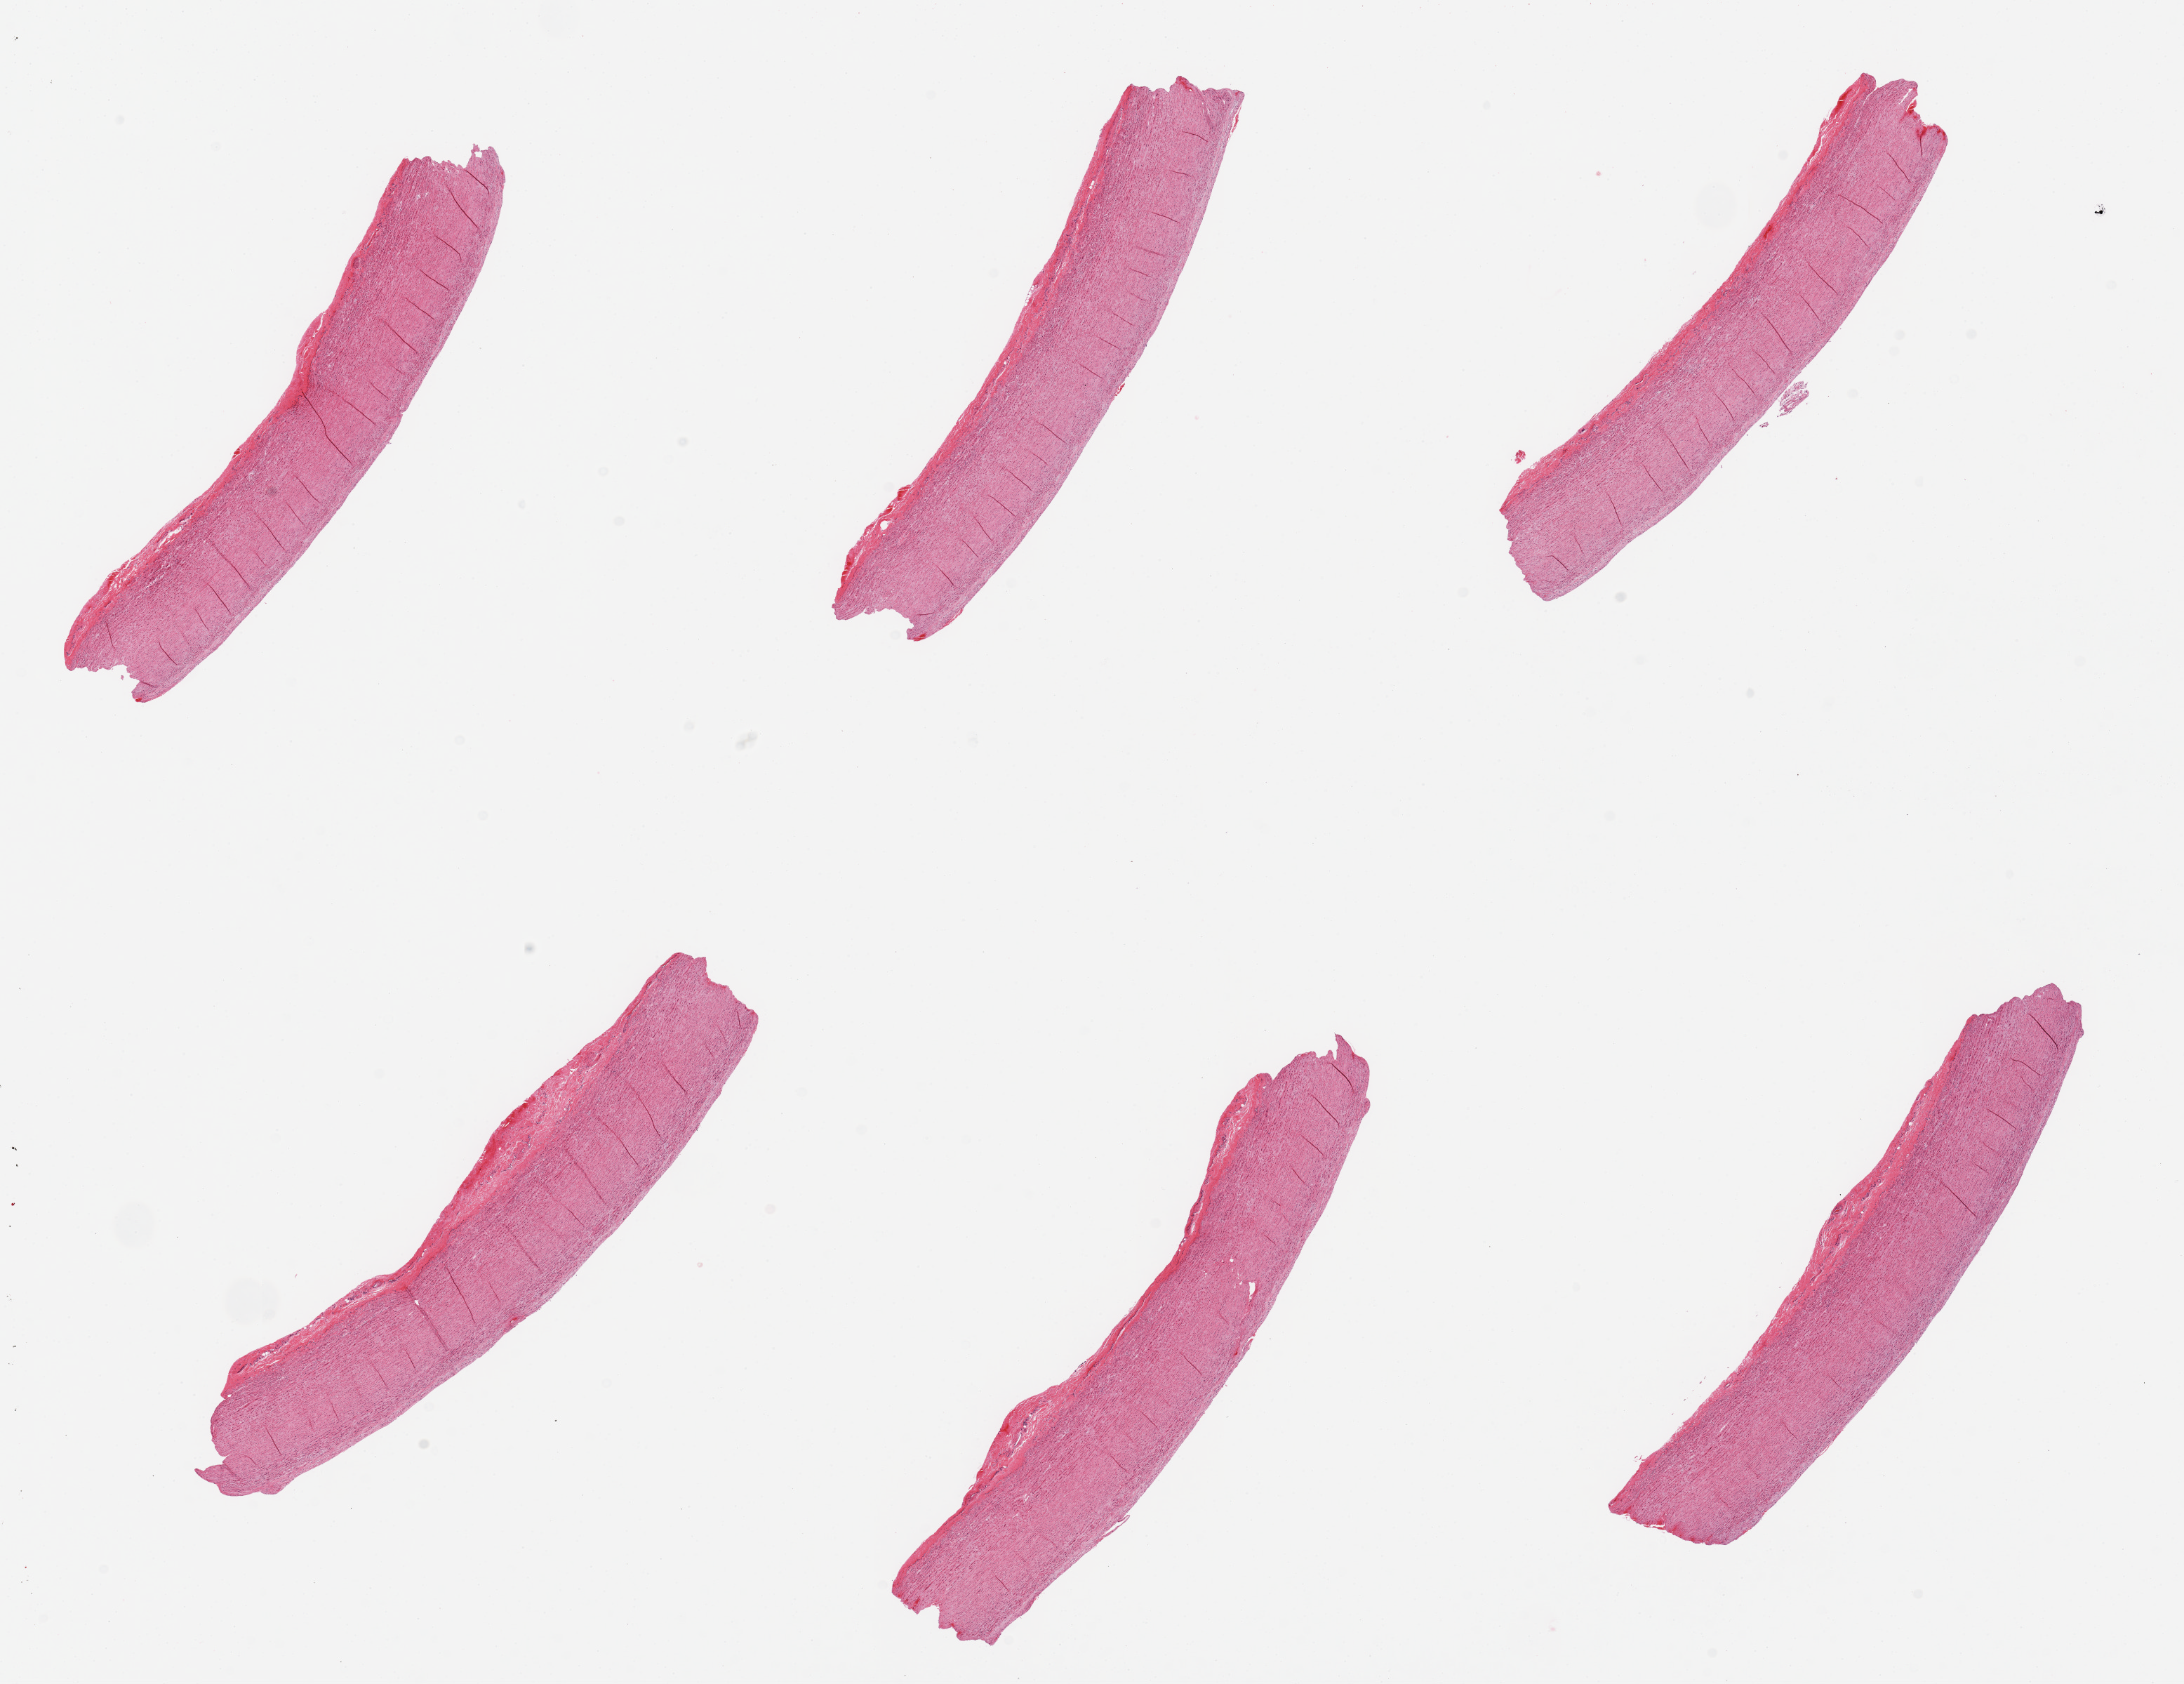
Digitized haematoxylin and eosin-stained section — a low-resolution overview of the entire scanned area, about 24.6 x 19.0 mm (acquisition: 20x scan). PAXgene-fixed, paraffin-embedded tissue. Sampled site (target tissue): aorta. Tissue donor sample.
* pathologist's review note for this sample: 6 pieces, minimal atherosis, adherent serosa up to ~0.5mm